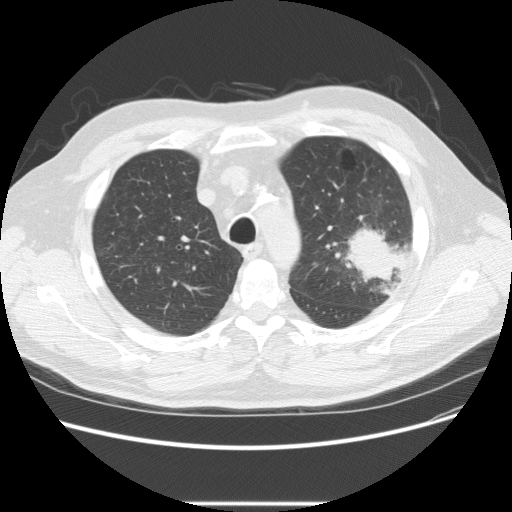
Chest CT (low-dose screening protocol), one axial image, baseline screening round, lung window (W 1500 / L -600 HU), 2.5 mm slice thickness, 120 kVp, slice 59 of 233 in the series, 512 × 512 image matrix, field of view 380 × 380 mm. Male participant, aged 73 years at enrolment. Former smoker at enrolment.
• Expert reader's lesion annotation, bounding box (x1, y1, x2, y2) in pixels: (332, 215, 415, 285).
• The screening reader recorded 2 non-calcified nodules or masses ≥4 mm on this exam; which of them this box marks is not recorded.
• Official screen result: positive, change unspecified: nodule(s) >= 4 mm or enlarging nodule(s), mass(es), or other non-specific abnormalities suspicious for lung cancer.
• Participant outcome: lung cancer diagnosed 11 days after this screen — bronchiolo-alveolar adenocarcinoma, NOS, other location, well differentiated (G1), stage IV (AJCC 6th edition).